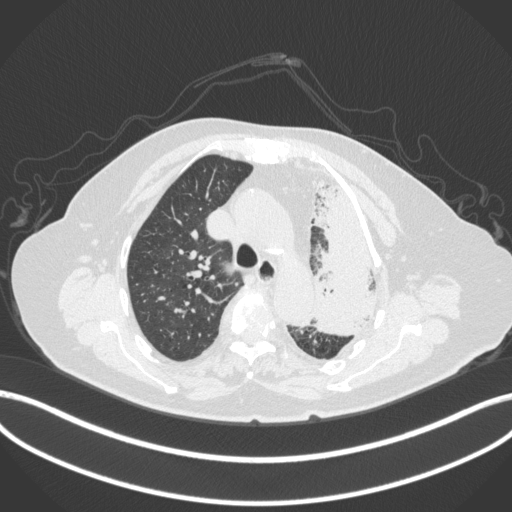
Chest CT, one axial slice. Position 287 of 399 along the scan axis. Reconstruction kernel B31f. 120 kVp. Lung window (W 1500 / L -600 HU). 512 × 512 image matrix. Female patient, age 75 years. Case-level facts recorded for this patient, not image findings: clinical TNM (as recorded): T3 N3 M1.
Structures marked on this image (bounding box drawn by a radiologist):
- lung tumour (recorded histology: adenocarcinoma): bounding box [x1, y1, x2, y2] px = [308, 173, 388, 339]